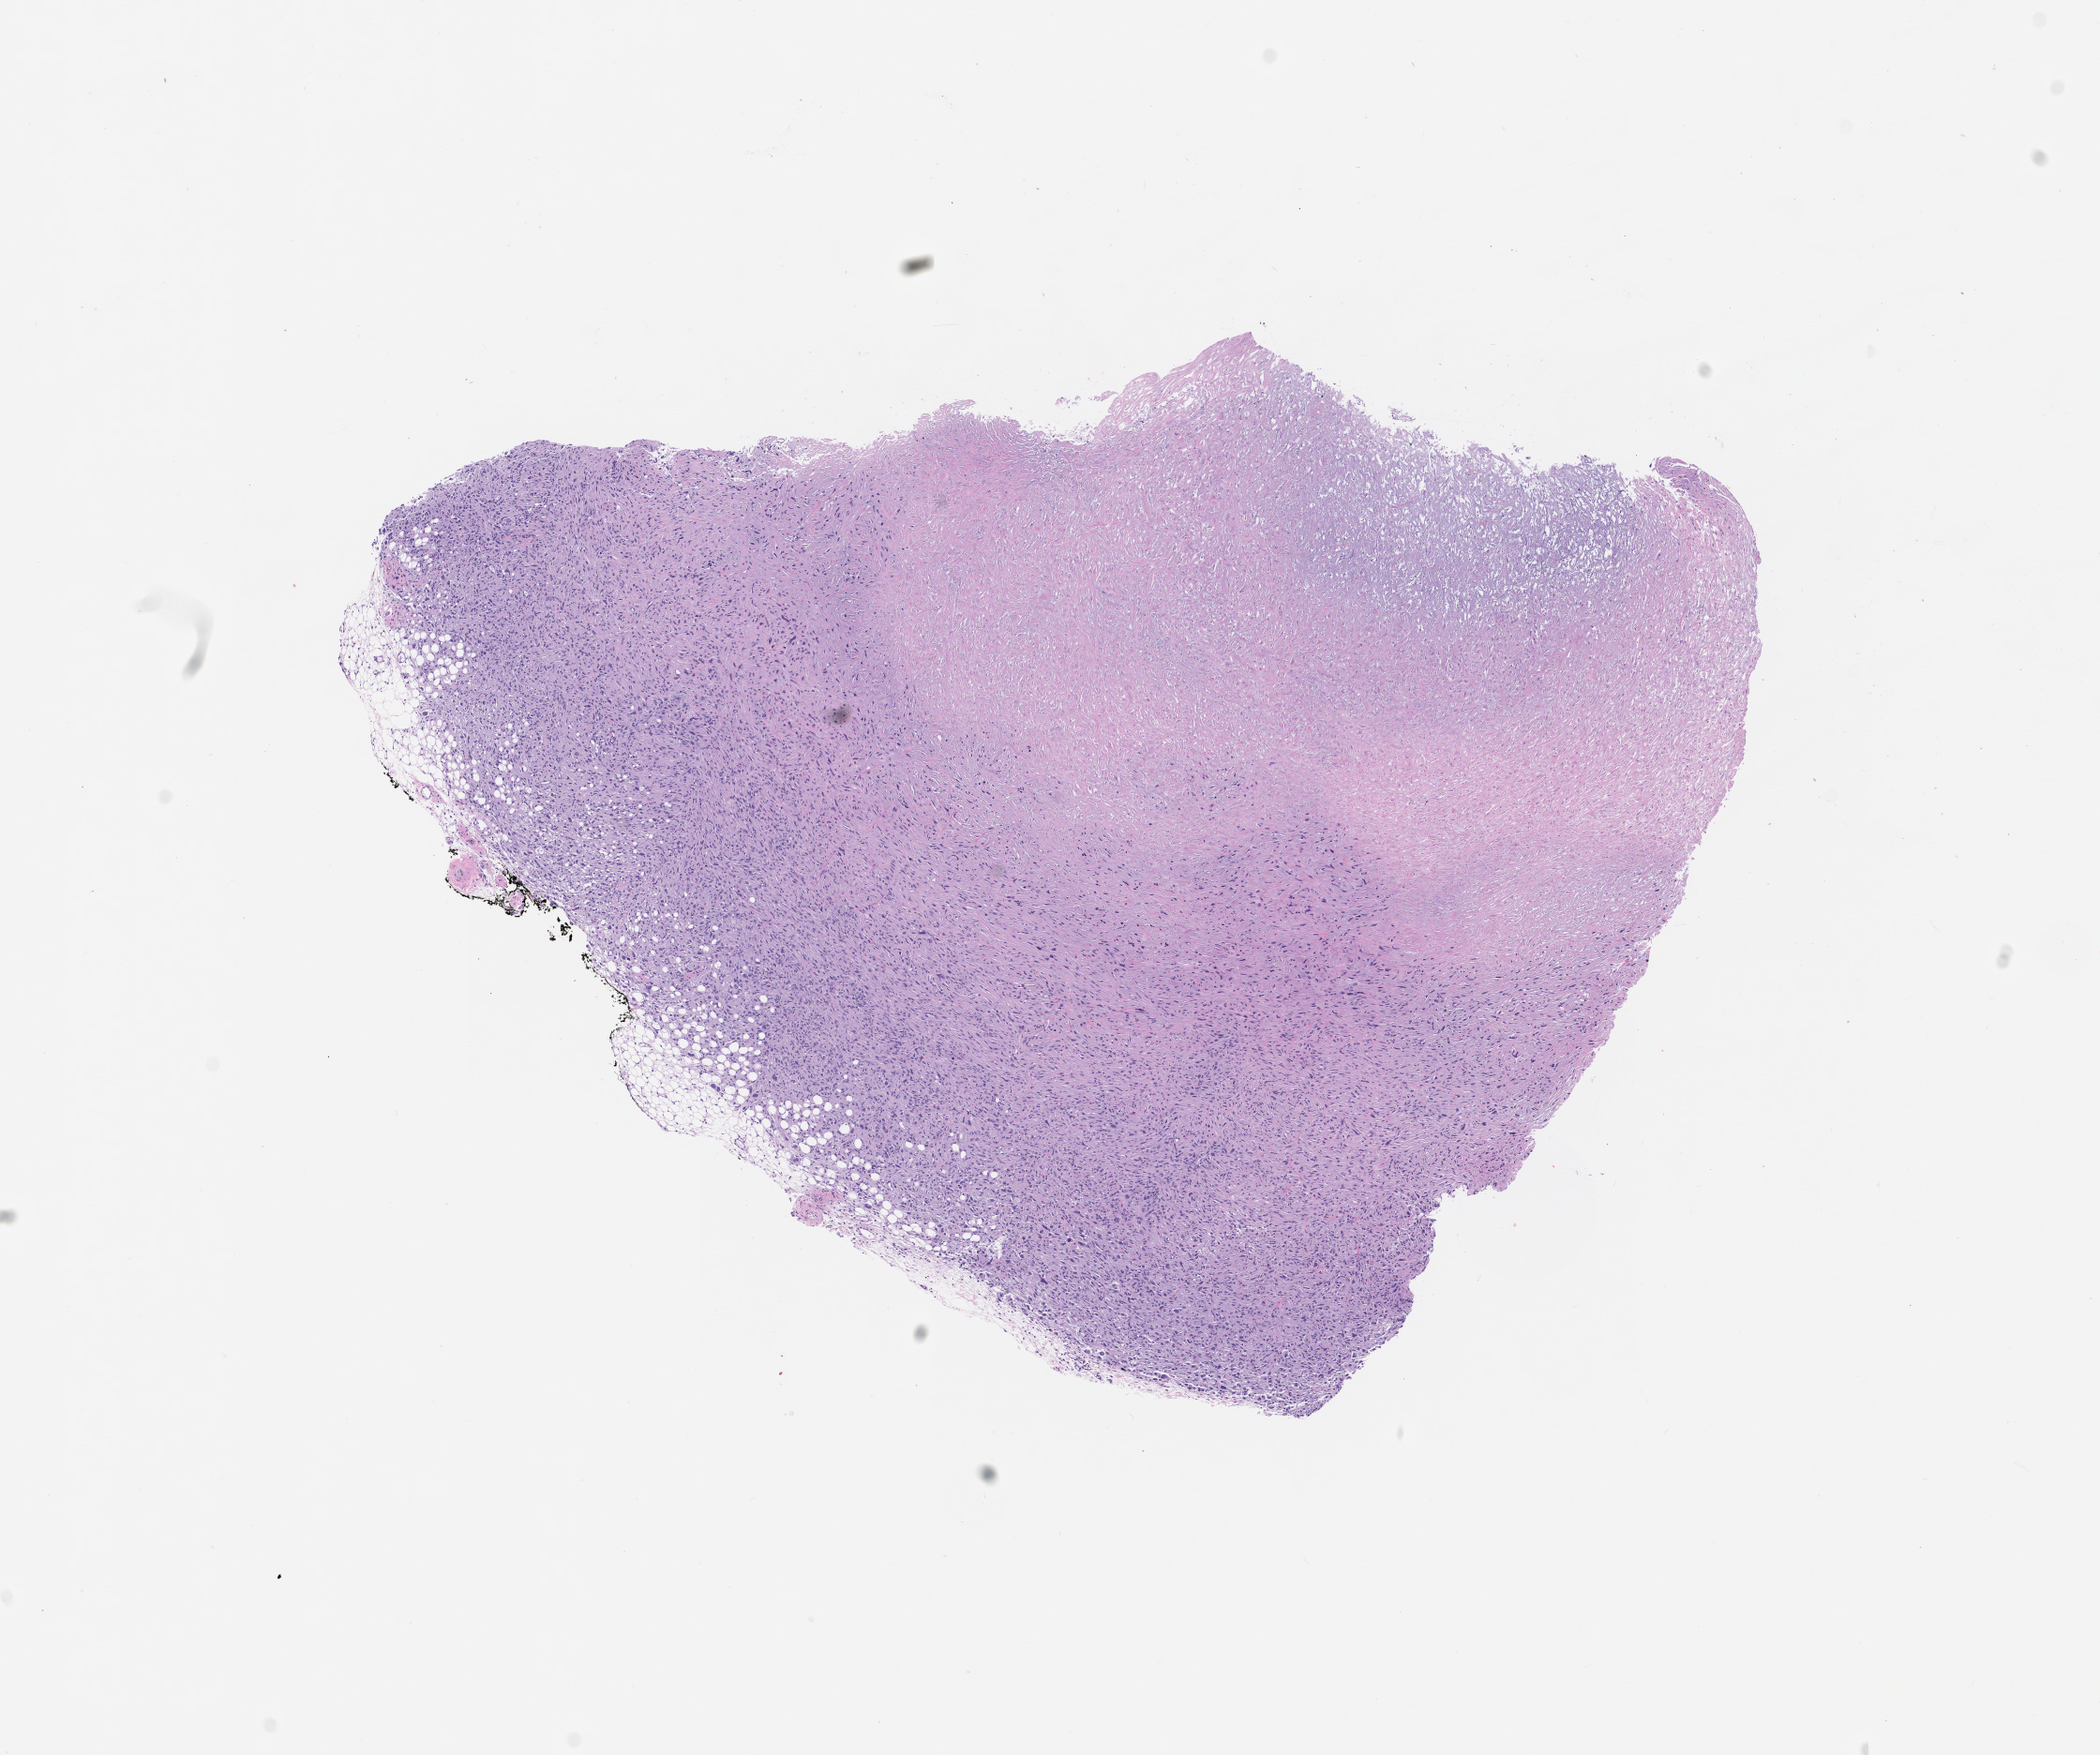
Hematoxylin and eosin (H&E) whole-slide image of a patient-derived xenograft (PDX) tumor grown in a mouse, shown as a low-resolution overview of the whole scanned area (about 9.0 x 7.5 mm); formalin-fixed paraffin-embedded section; originating tumor site category: musculoskeletal.
* originating patient diagnosis: Spindle Cell Sarcoma